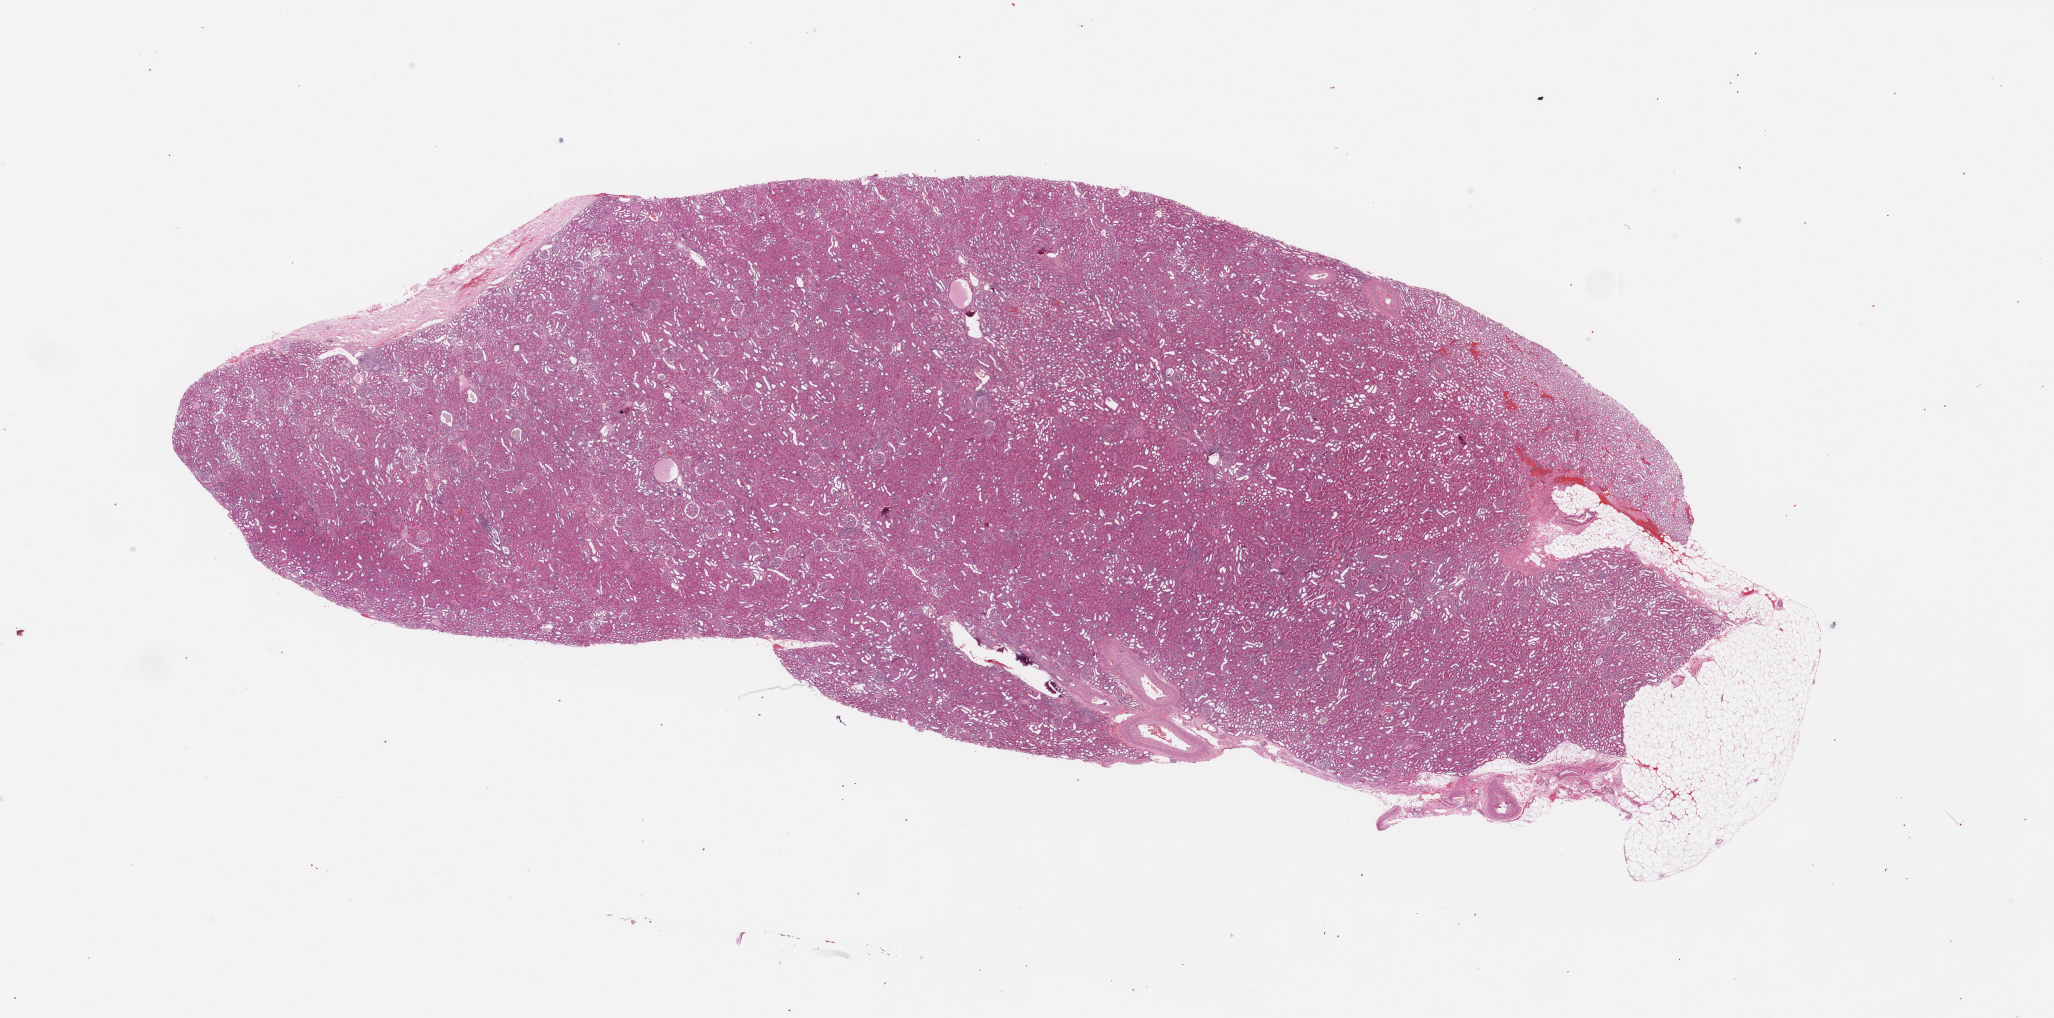
H&E whole-slide image, a low-resolution overview of the entire scanned area, about 32.5 x 16.1 mm (acquisition: 20x scan), normal (non-tumour) tissue sample, kidney. 59-year-old female patient.
This section: normal (non-tumour) tissue from the same patient. Patient diagnosis: Renal cell carcinoma, NOS.